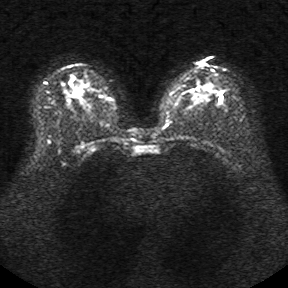
Breast MRI, one axial slice. Slice 22 of 34 in the series (ordered by position). Diffusion-weighted series; image 2 of 4 stored at this slice position (different b-values; order by instance number). 1.5 T. 5 mm slice thickness. 288 × 288 image matrix, field of view 340 × 340 mm. Female patient.
Outlined on this slice (outlined manually by an expert reader):
- tumour on diffusion-weighted imaging: bounding box (x1, y1, x2, y2) in pixels: (202, 85, 211, 91)